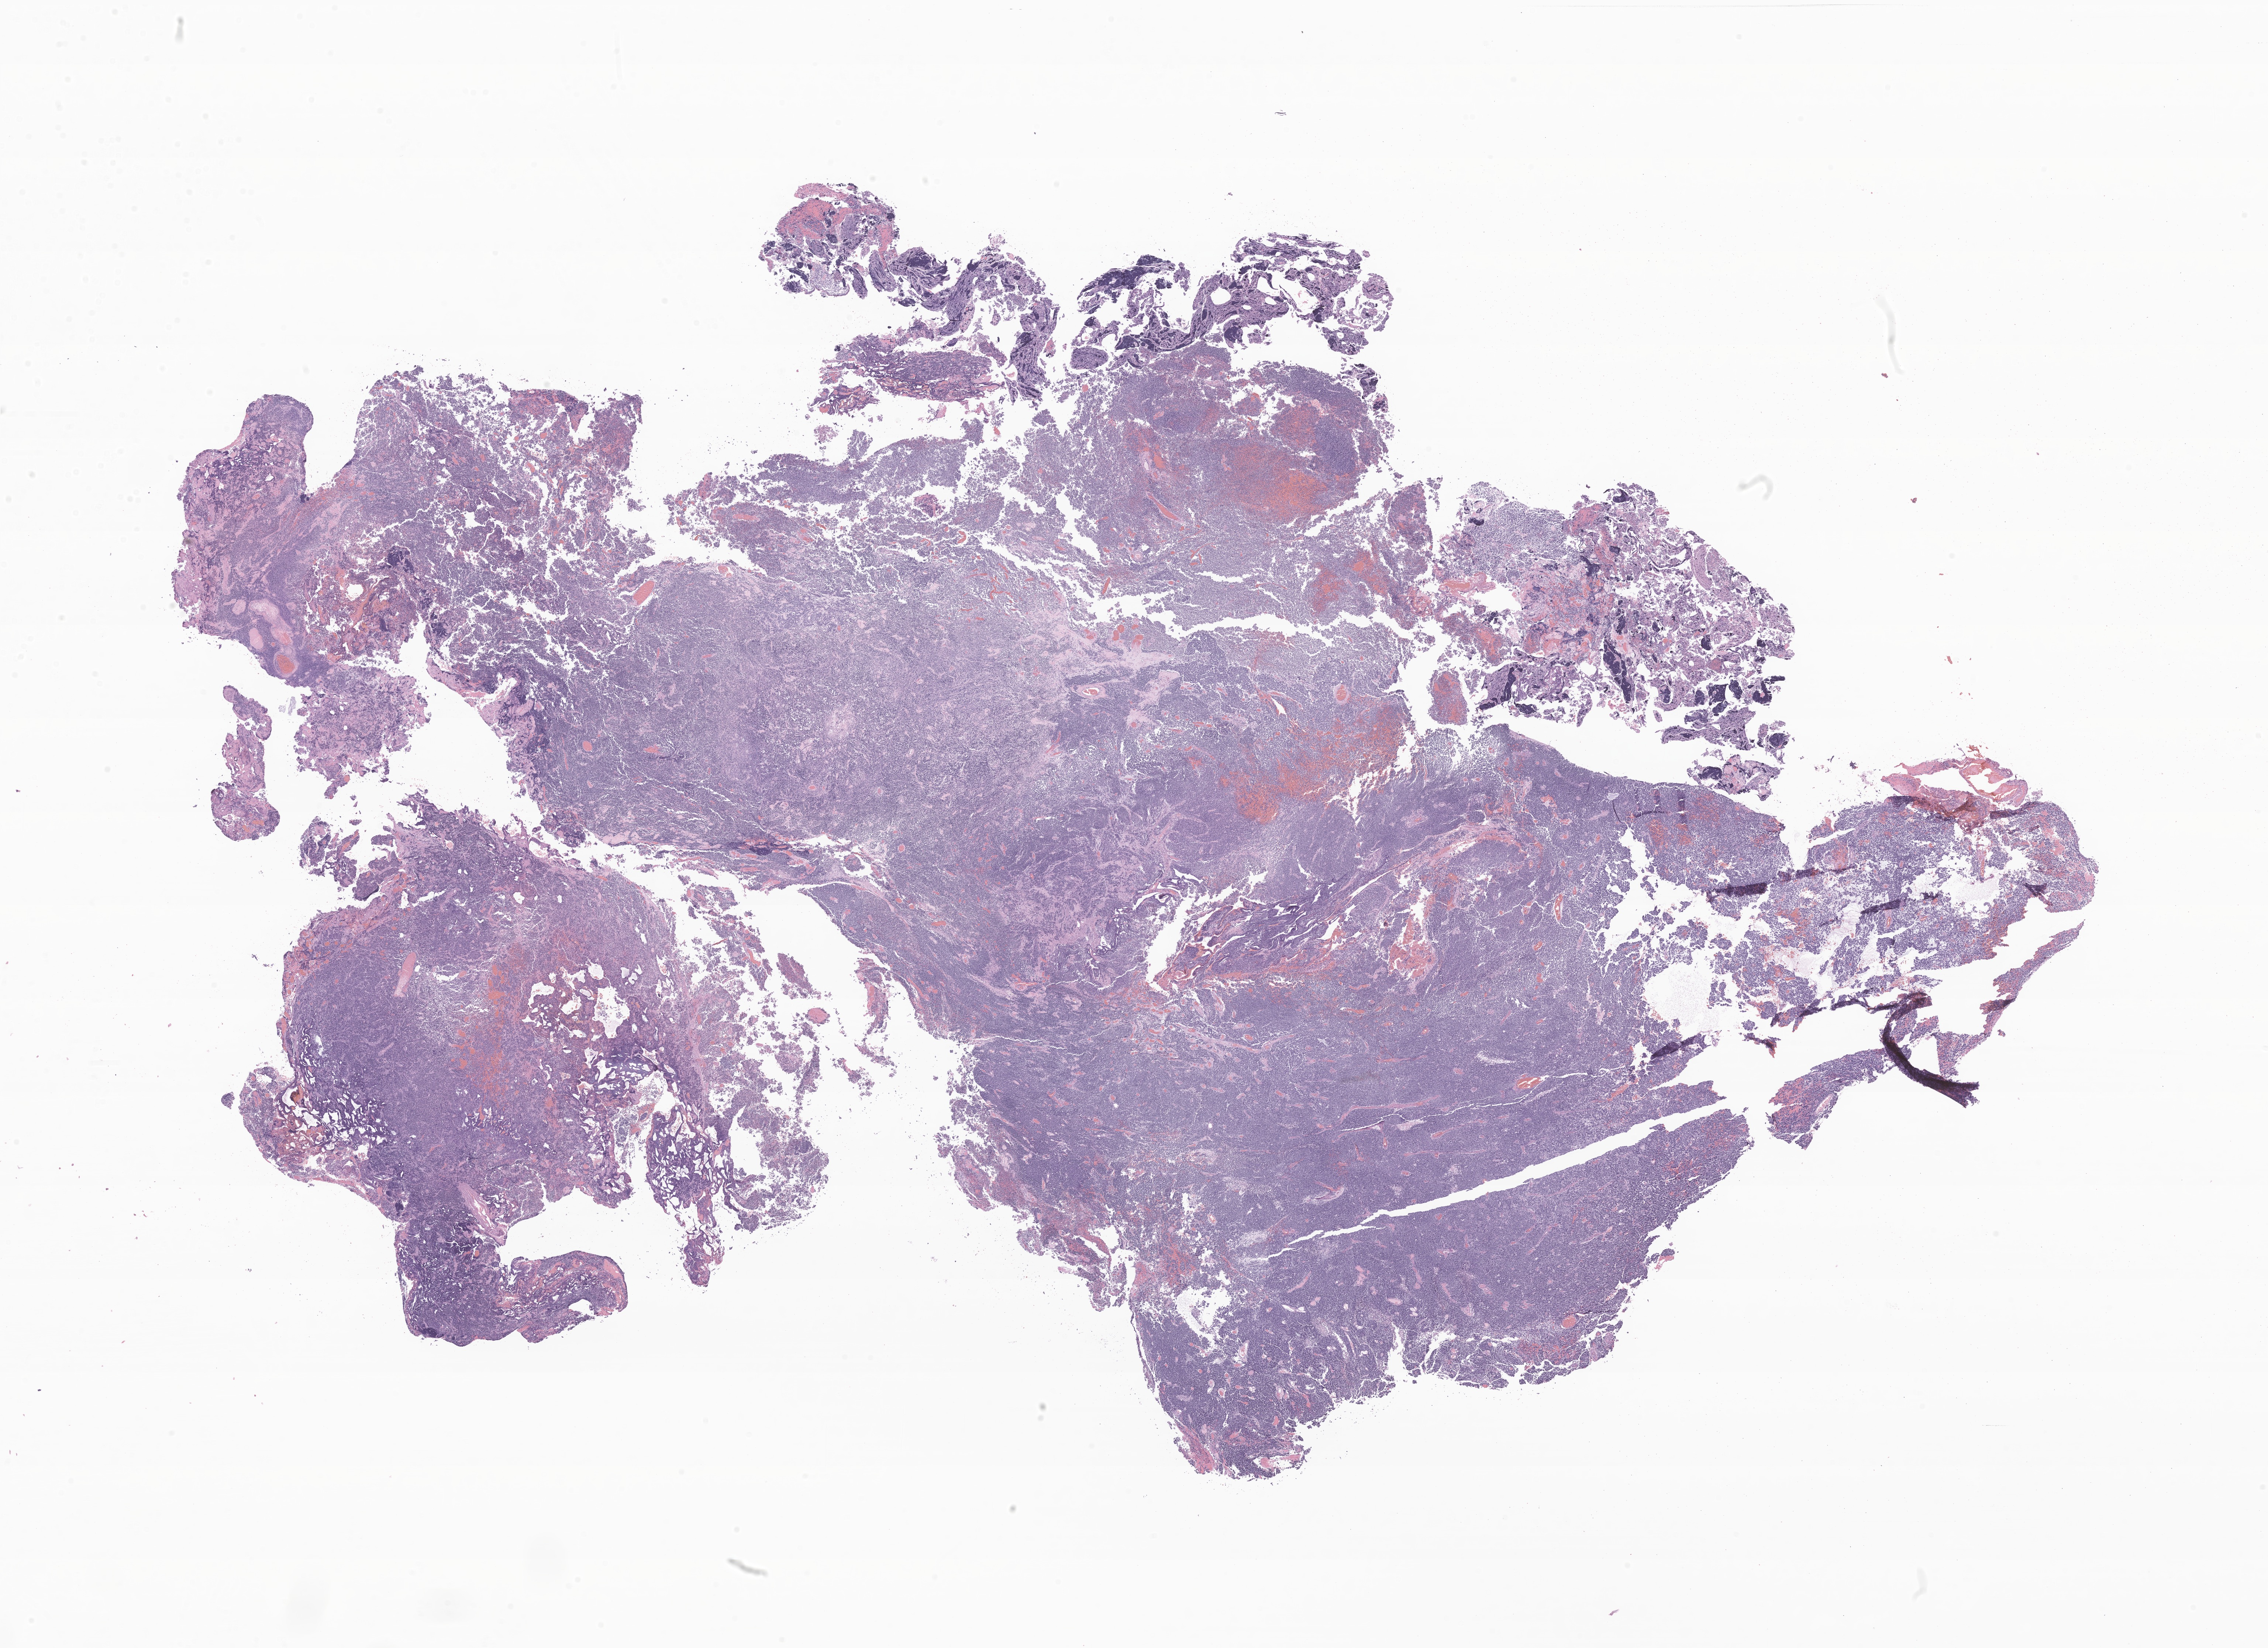
Whole-slide image, hematoxylin and eosin (H&E) stain of tumor tissue from the brain, shown as a low-resolution overview of the whole scanned area (about 25.9 x 18.8 mm), FFPE section. Male patient, age 66 months (5 years 6 months).
Diagnosis: Neoplasm, malignant.